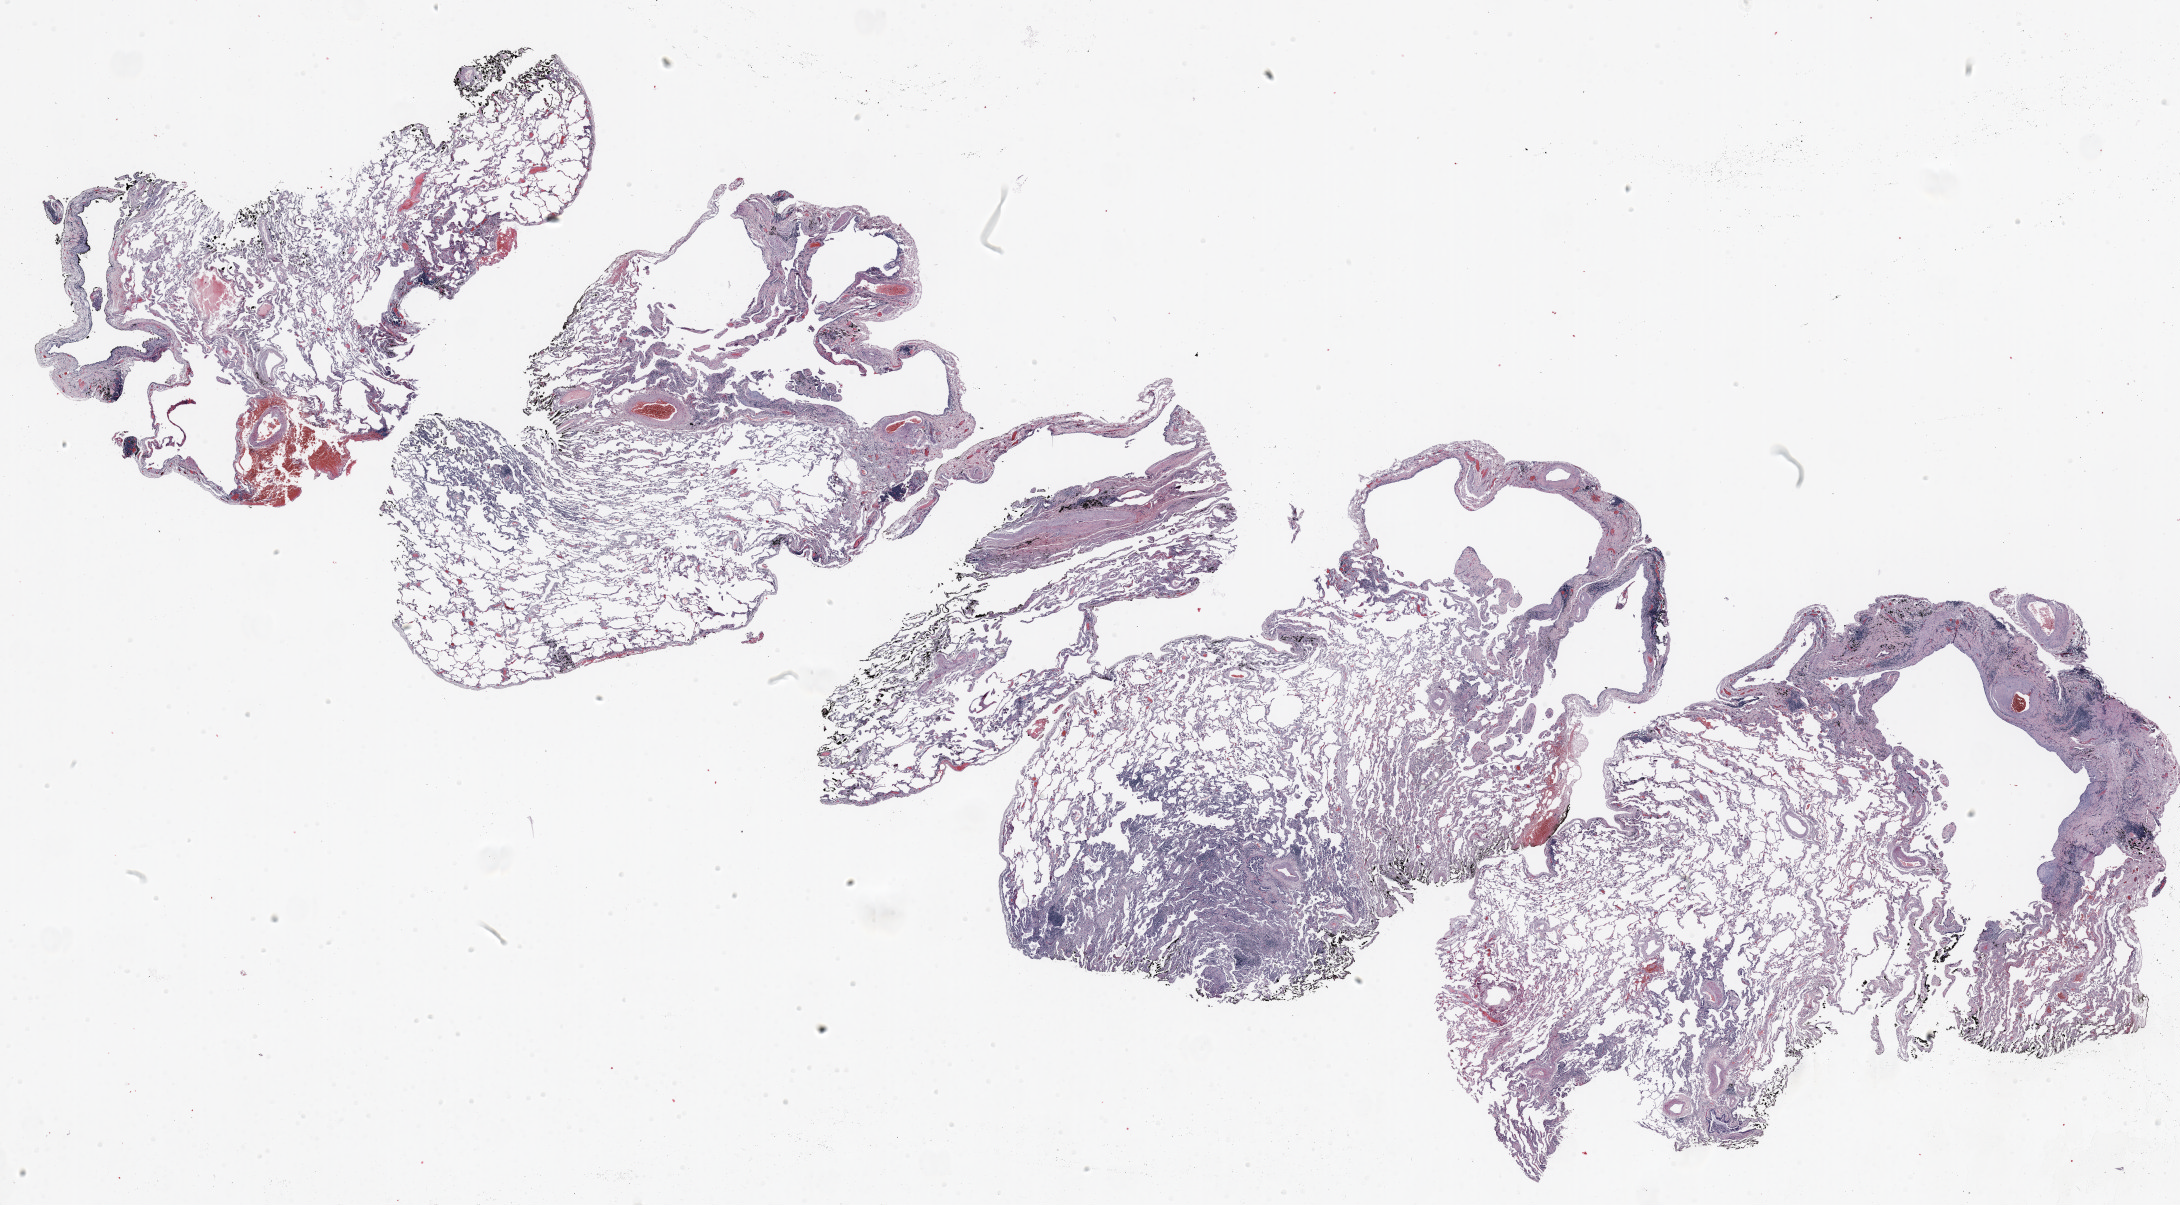
H&E whole-slide image — shown as a low-resolution overview of the whole scanned area (about 35.0 x 19.4 mm, acquisition: 20x scan); FFPE section; lung tissue. Female, age 74 at enrolment. Current smoker at enrolment. Grade: poorly differentiated (G3).
* tumour size (pathology): 18 mm
* stage (AJCC 6th edition): IV
* primary tumour location (clinical record): other location
* participant's lung-cancer diagnosis: Bronchiolo-alveolar adenocarcinoma, NOS